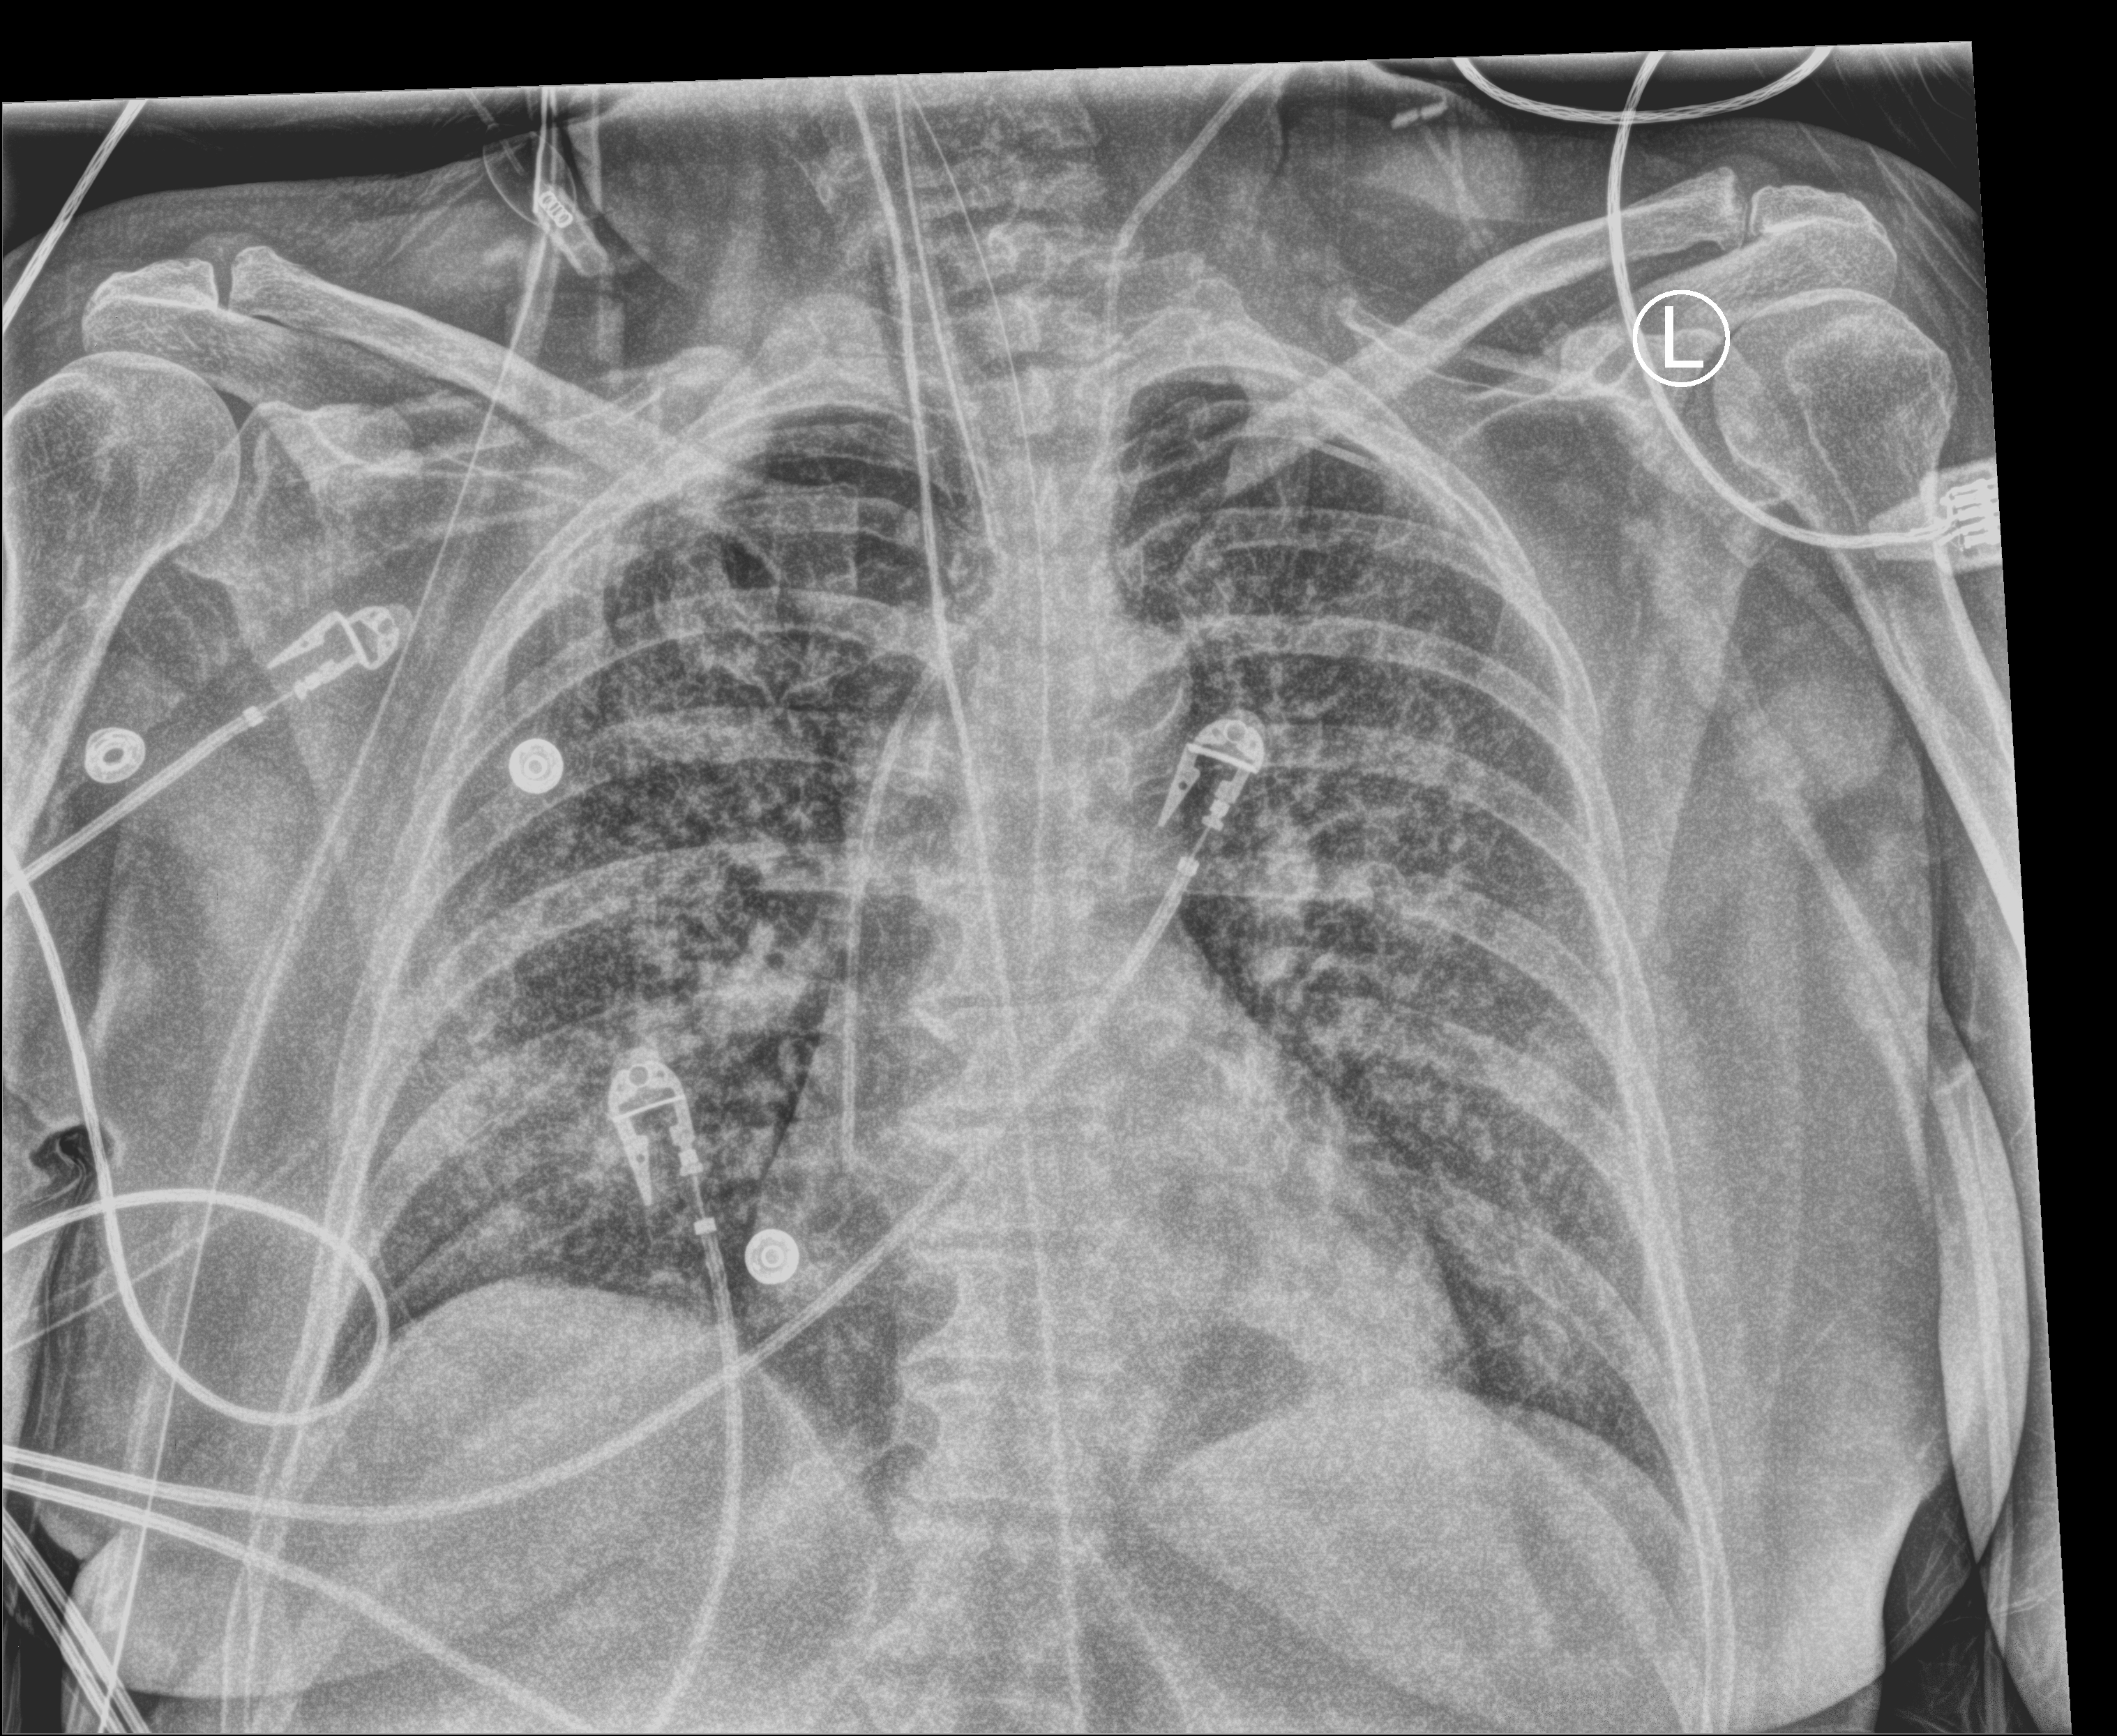
Bedside chest radiograph (computed radiography), anteroposterior (AP) projection. Patient hospitalised with COVID-19; female, aged 60–74 years.
Admission-level facts for this patient (not findings on this image; timing relative to this image not recorded):
- admitted to intensive care during this hospital stay: yes
- length of hospital stay: 24 days
- mechanically ventilated during this hospital stay: yes